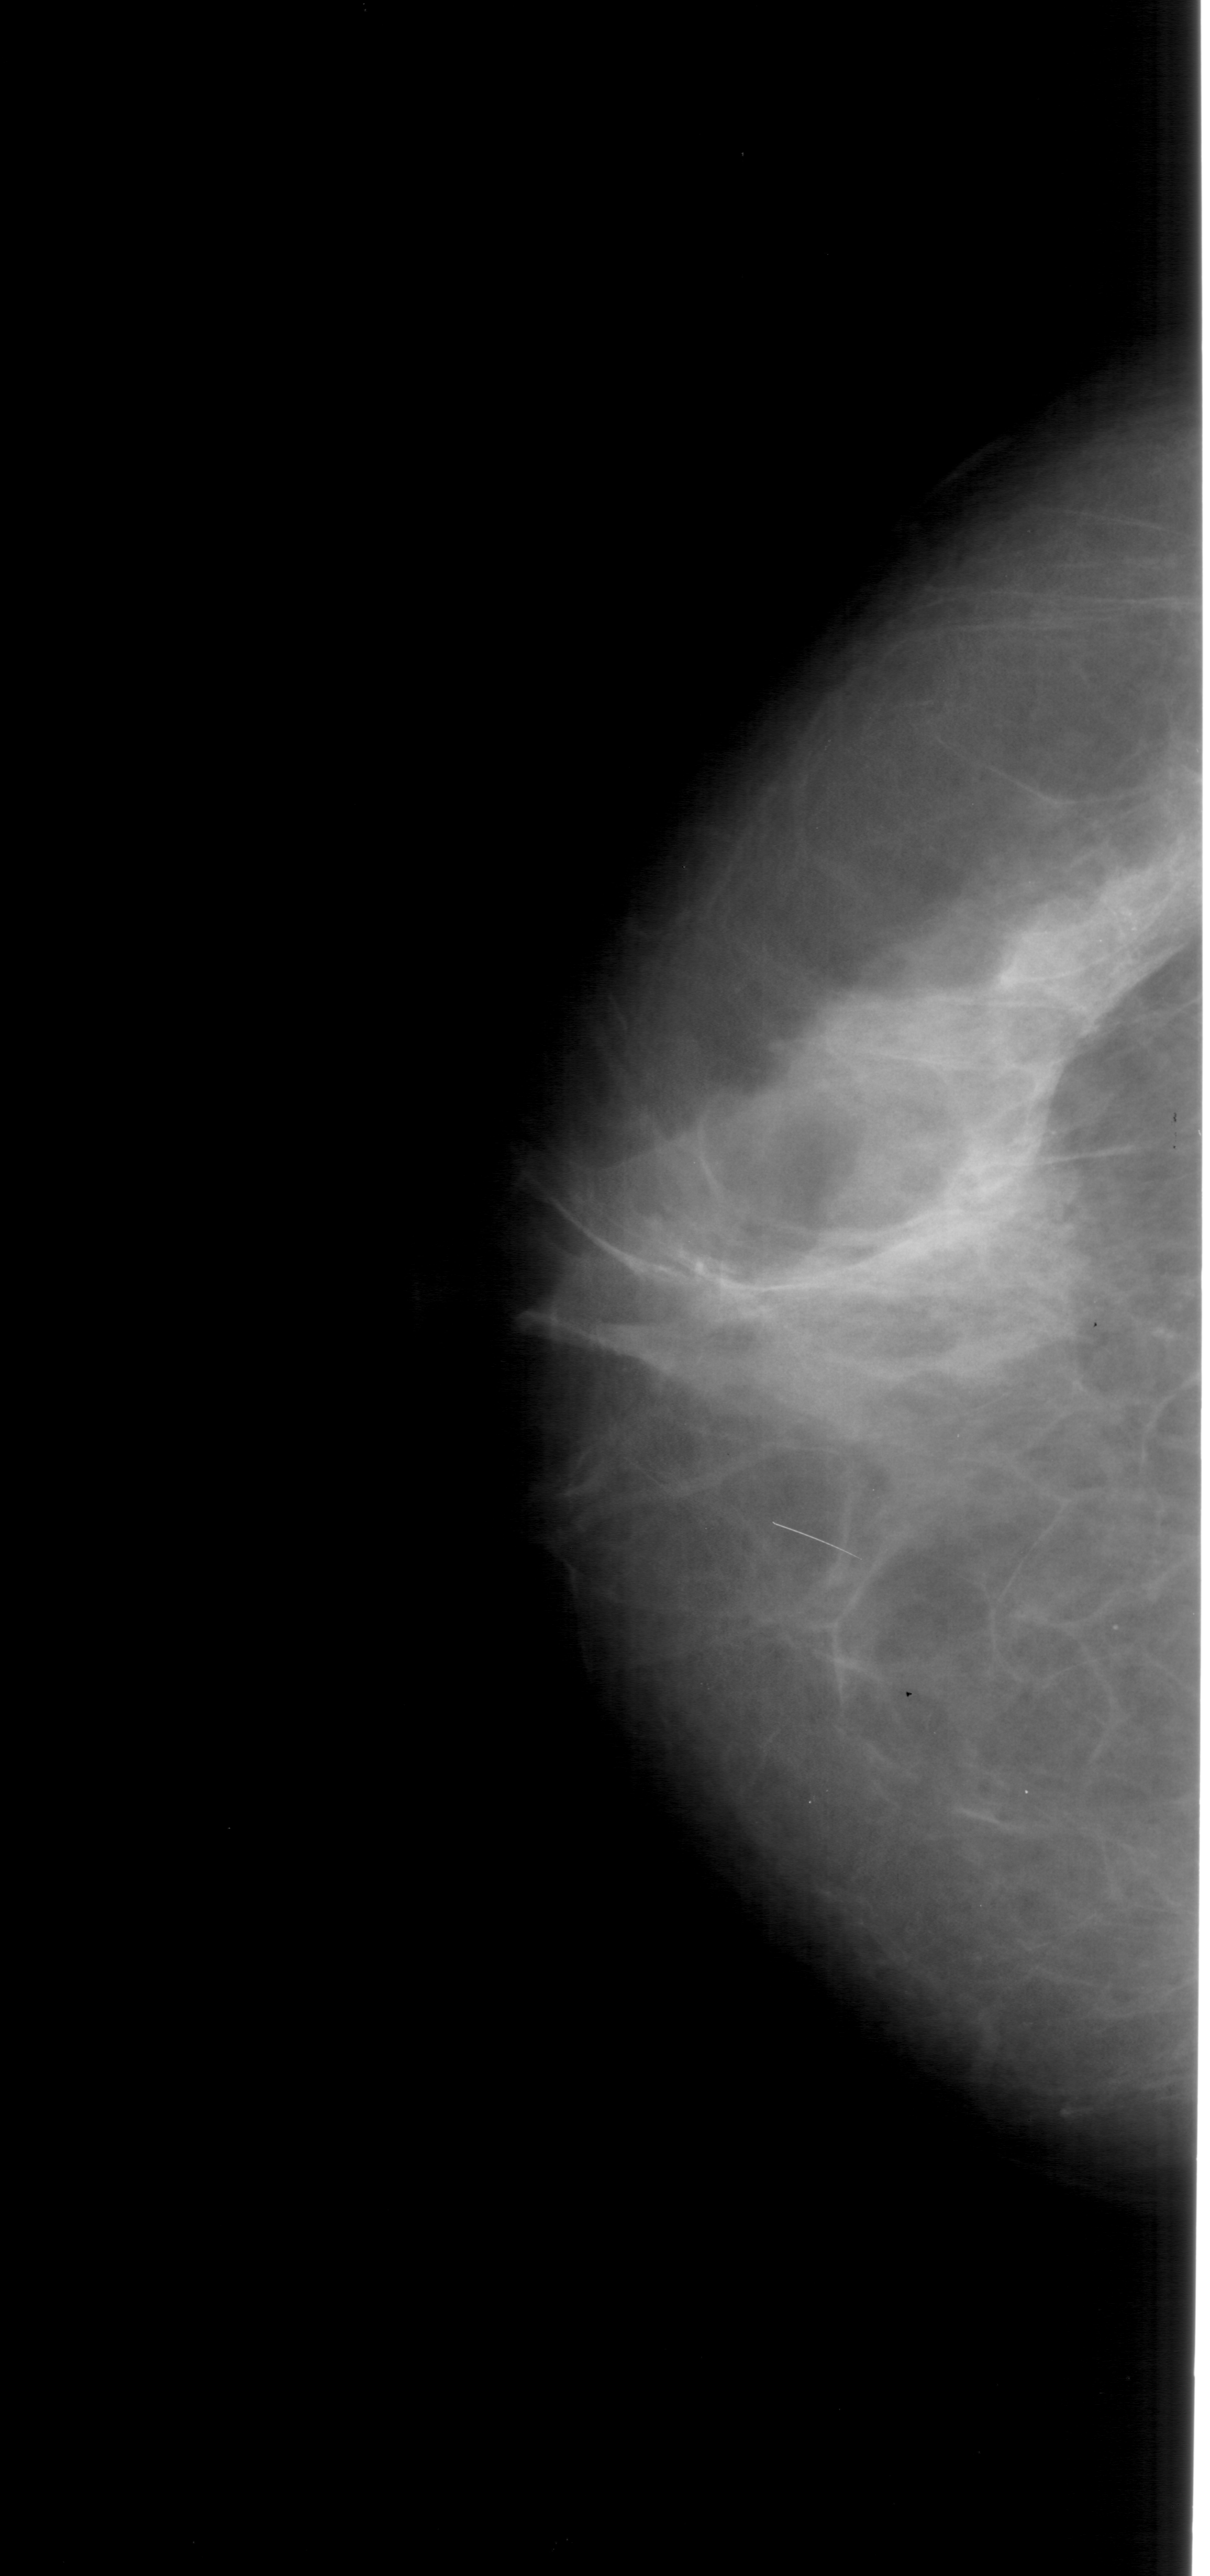
Digitized screen-film mammogram, left breast, craniocaudal (CC) view, BI-RADS breast density category 4 (scale 1–4).
- Calcifications, morphology pleomorphic, distribution clustered; BI-RADS assessment category 4; subtlety rating 3 on a 1 (subtle) to 5 (obvious) scale; pathology (as recorded): benign.